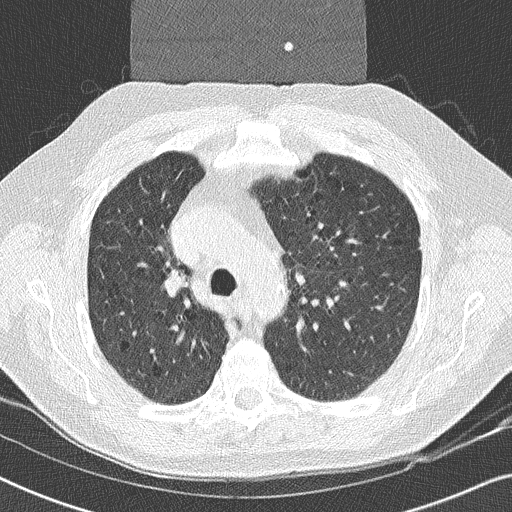
Chest CT (low-dose screening protocol), one axial image. Second annual screen. Lung window (W 1500 / L -600 HU). 2 mm slice thickness. Male, age 59 years at enrolment. Former smoker at enrolment.
- Lesion marked by an expert reader, bounding box (x1, y1, x2, y2) in pixels: (140, 255, 202, 308).
- Screening reader's record for this exam (one nodule recorded; not confirmed to be the boxed lesion): non-calcified nodule or mass ≥4 mm, right upper lobe, 17 × 16 mm, smooth margins, soft tissue attenuation, pre-existing on the prior screen: yes.
- Official screen result: positive, other.
- Later outcome: lung cancer diagnosed 14 days after this screen — squamous cell carcinoma, NOS, right upper lobe, poorly differentiated (G3), stage IIA (AJCC 6th edition), 20 mm at pathology.